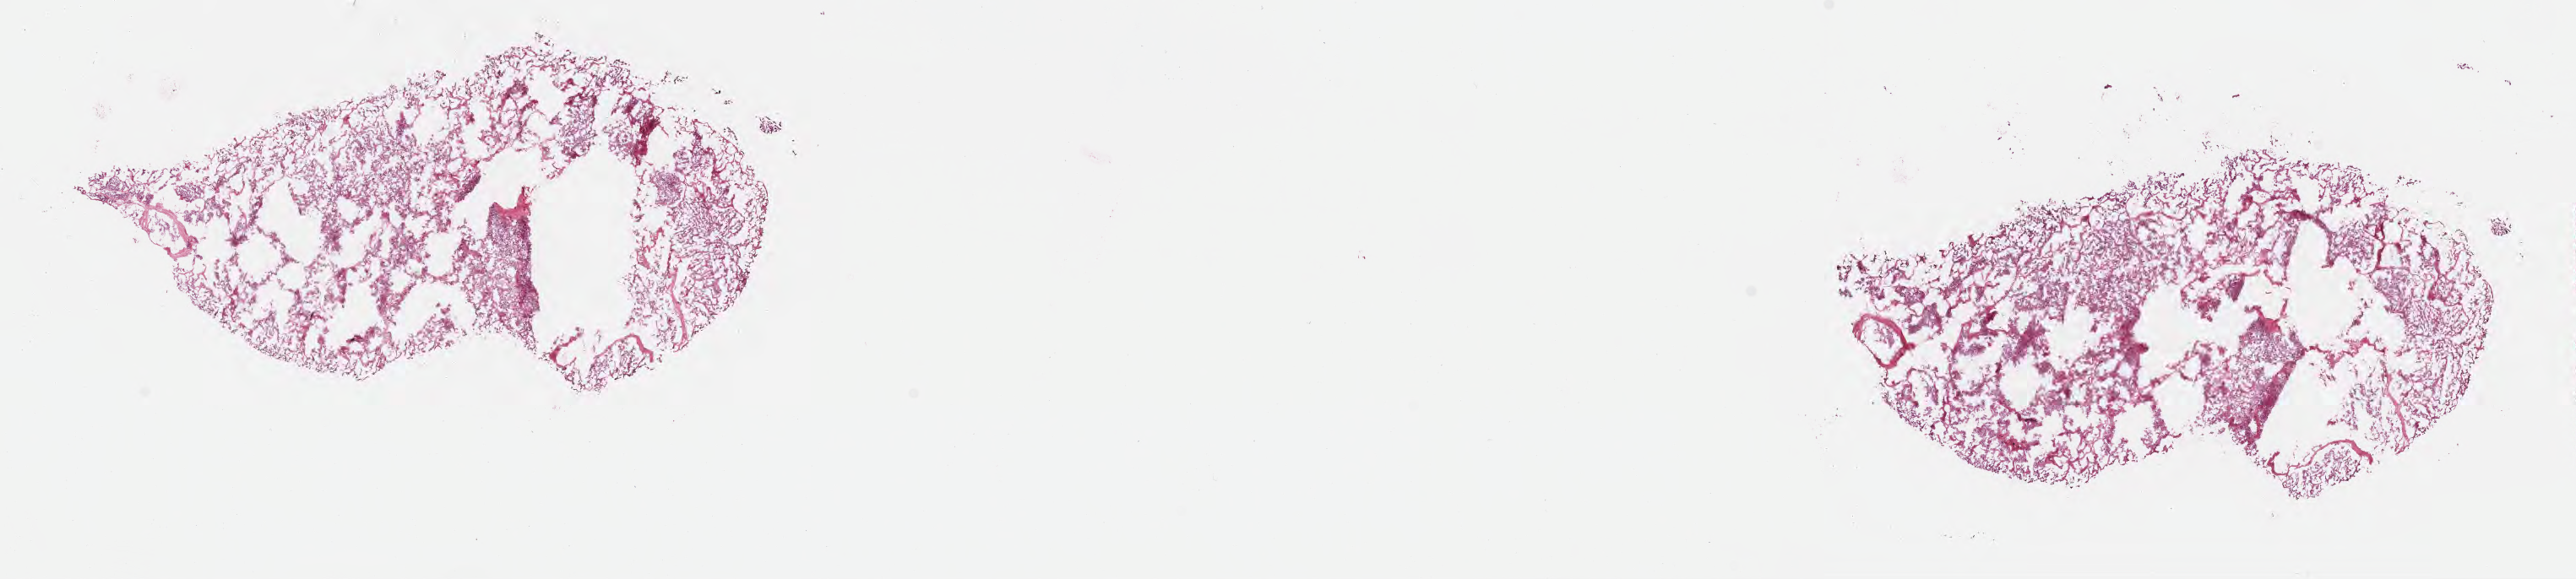
Hematoxylin and eosin (H&E) whole-slide image, shown as a low-resolution overview of the whole scanned area (about 24.7 x 5.5 mm). Frozen section. Primary tumor. Anatomic site: kidney. Patient: male, age at initial diagnosis 63 years.
Histologic diagnosis: Renal cell carcinoma, chromophobe type.